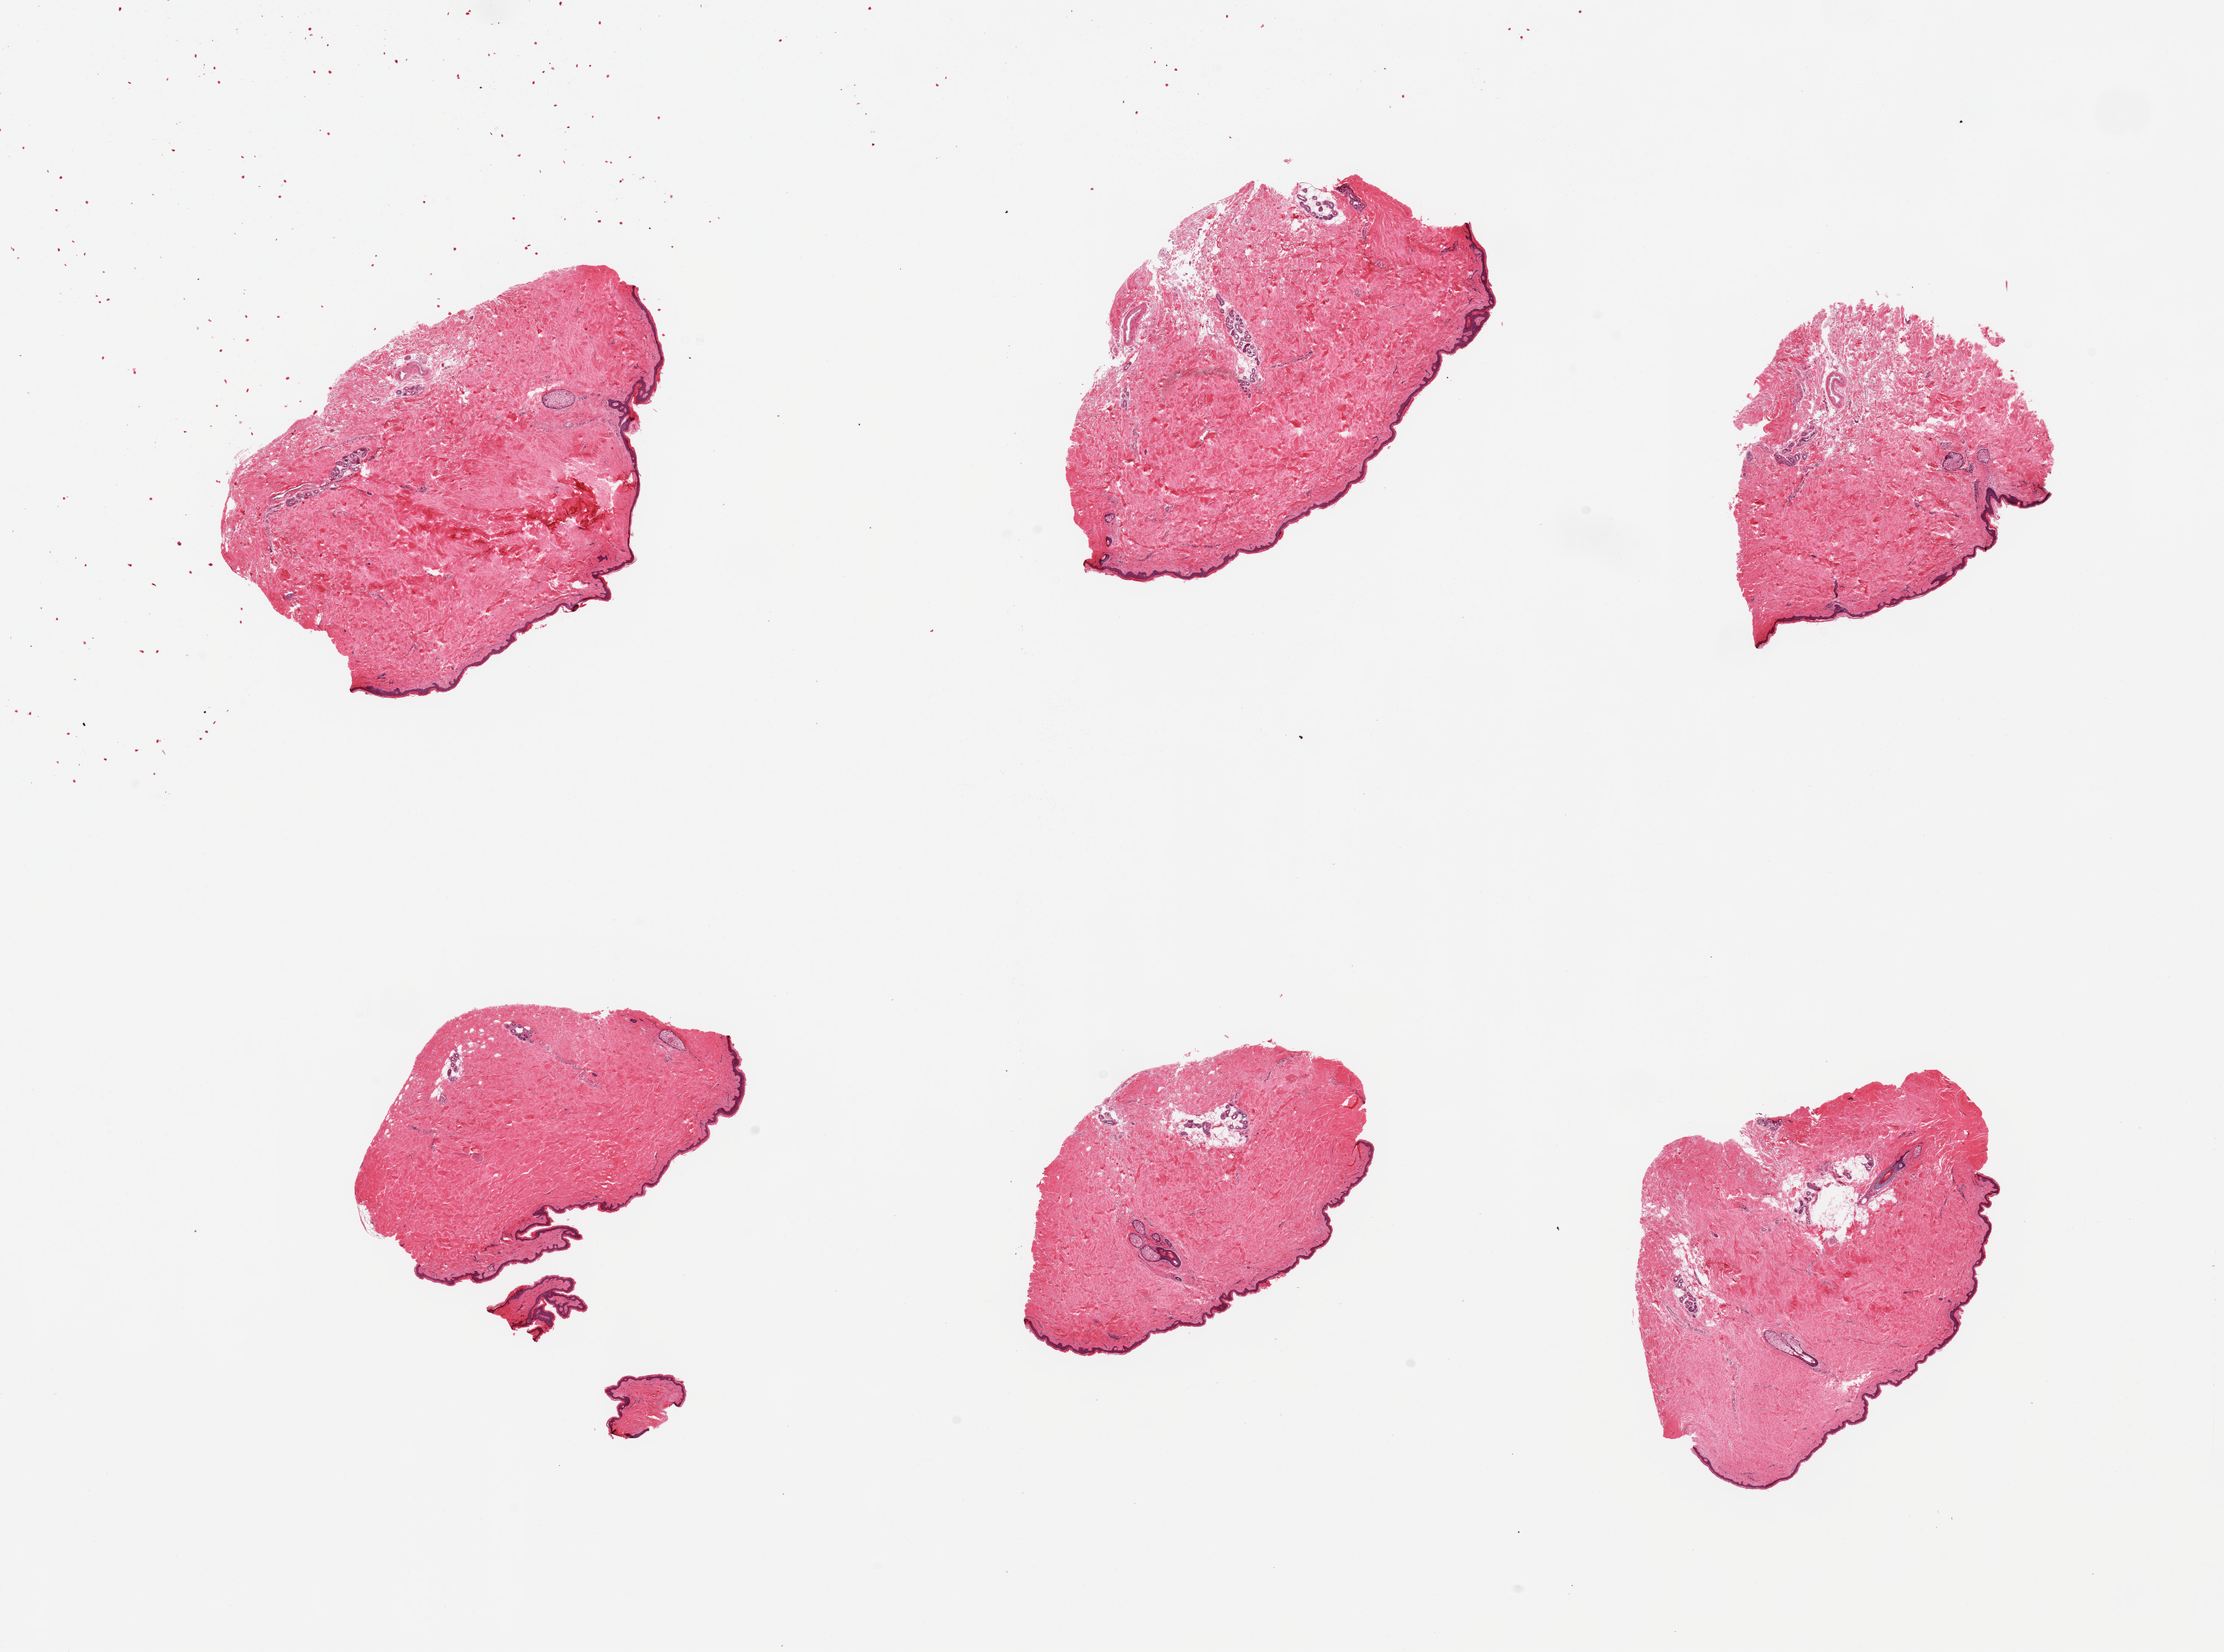
H&E whole-slide image — low-resolution overview of the scanned area, about 23.6 x 17.6 mm, PAXgene-fixed, paraffin-embedded tissue, target tissue: skin of suprapubic region, tissue donor sample. Female donor.
Review note (as recorded): 6 pieces; well trimmed.